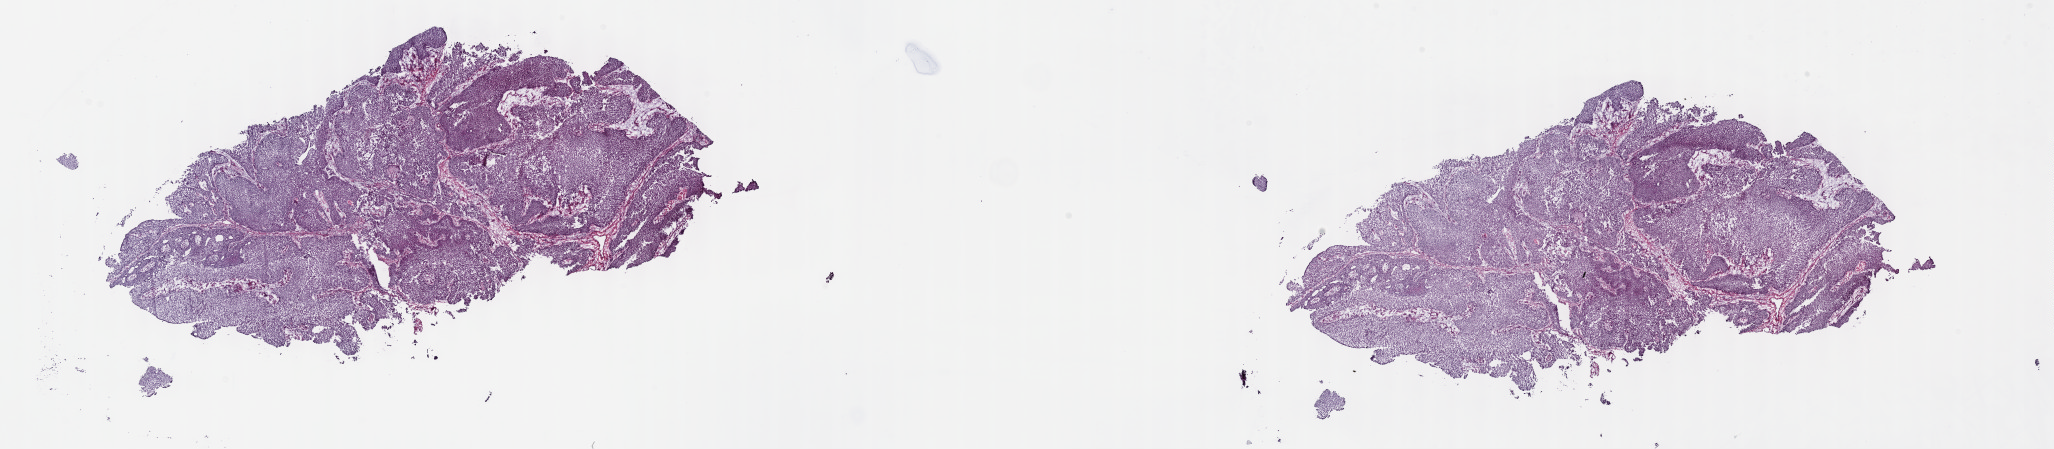
H&E-stained whole-slide image — a low-resolution overview of the entire scanned area, about 33.2 x 7.3 mm (acquisition: 40x scan); frozen section from the top of the tissue portion; sample: primary tumour, bladder. Patient: female, age at initial diagnosis 57 years. Histologic grade: high grade. Pathologist review of this section (percent, as recorded): tumour cells 90%, tumour nuclei 95%, normal cells 0%, stromal cells 10%, necrosis 0%. Inflammatory infiltration, as recorded: lymphocyte infiltration 0%, monocyte infiltration 0%, neutrophil infiltration 0%.
• diagnosis: Papillary transitional cell carcinoma
• AJCC pathologic stage: IV (6th edition)
• lymph nodes positive (case pathology): 32 of 61 examined